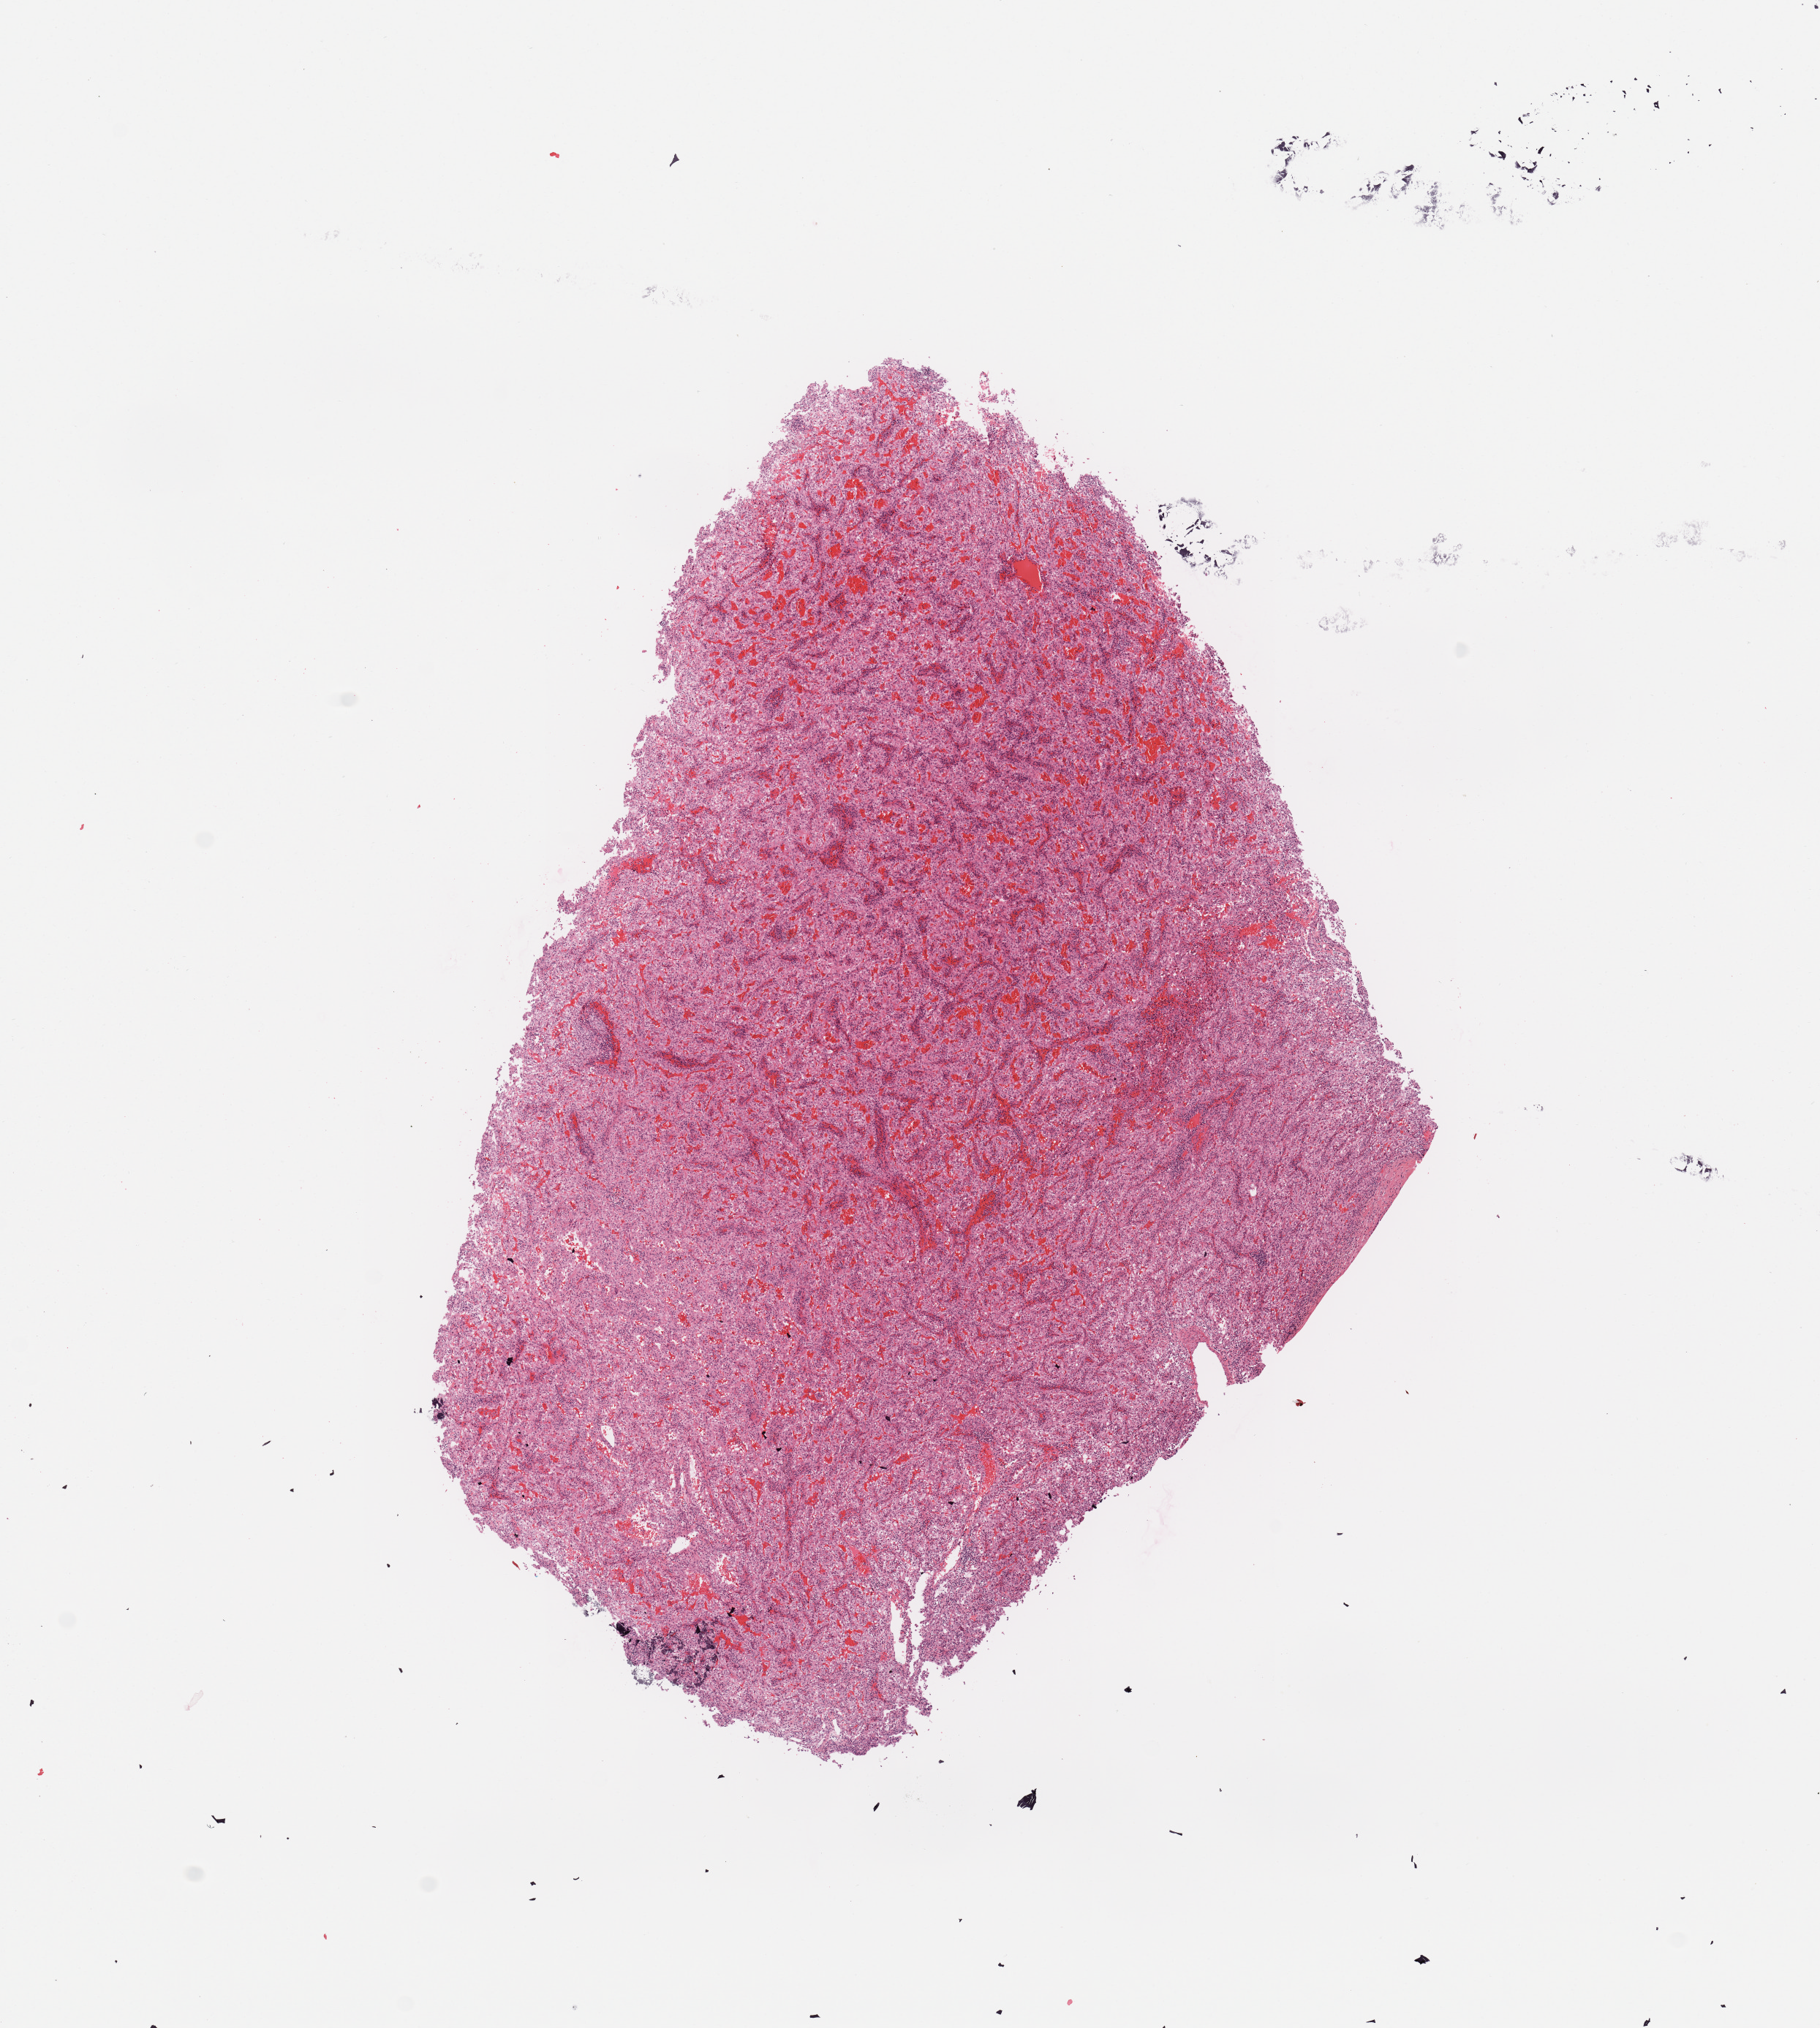
Hematoxylin and eosin (H&E) stained whole-slide image — whole scanned area (about 9.8 x 11.0 mm) shown as a low-resolution overview; tumour tissue sample, sampled site: kidney. Male, 41 y/o. Slide review estimates, as recorded: tumour nuclei 85%, necrosis 0%.
Histologic diagnosis: Renal cell carcinoma, NOS.